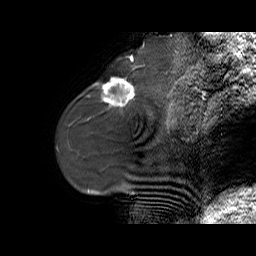
Breast MRI (dynamic contrast-enhanced), one sagittal slice. Position 18 of 70 along the scan axis. Dynamic contrast-enhanced series, time point 2 of 6 at this slice position (early post-contrast). 1.5 T. TE 5.5 ms, TR 32.9 ms. 4 mm slice thickness. 256 × 256 image matrix, field of view 240 × 240 mm. Female patient. Case-level facts recorded for this patient, not image findings: setting: breast cancer imaged before/during neoadjuvant chemotherapy; receptor status: HER2-positive.
Annotated regions visible in this slice (semi-automatically segmented with operator editing):
- analysis volume of interest (the breast-tissue region the enhancement analysis was run in; not a lesion): bounding box [x1, y1, x2, y2] px = [96, 73, 141, 114]
- tumour enhancement mask (voxels above the 100 % enhancement threshold inside the analysis volume of interest): [102, 79, 135, 105]